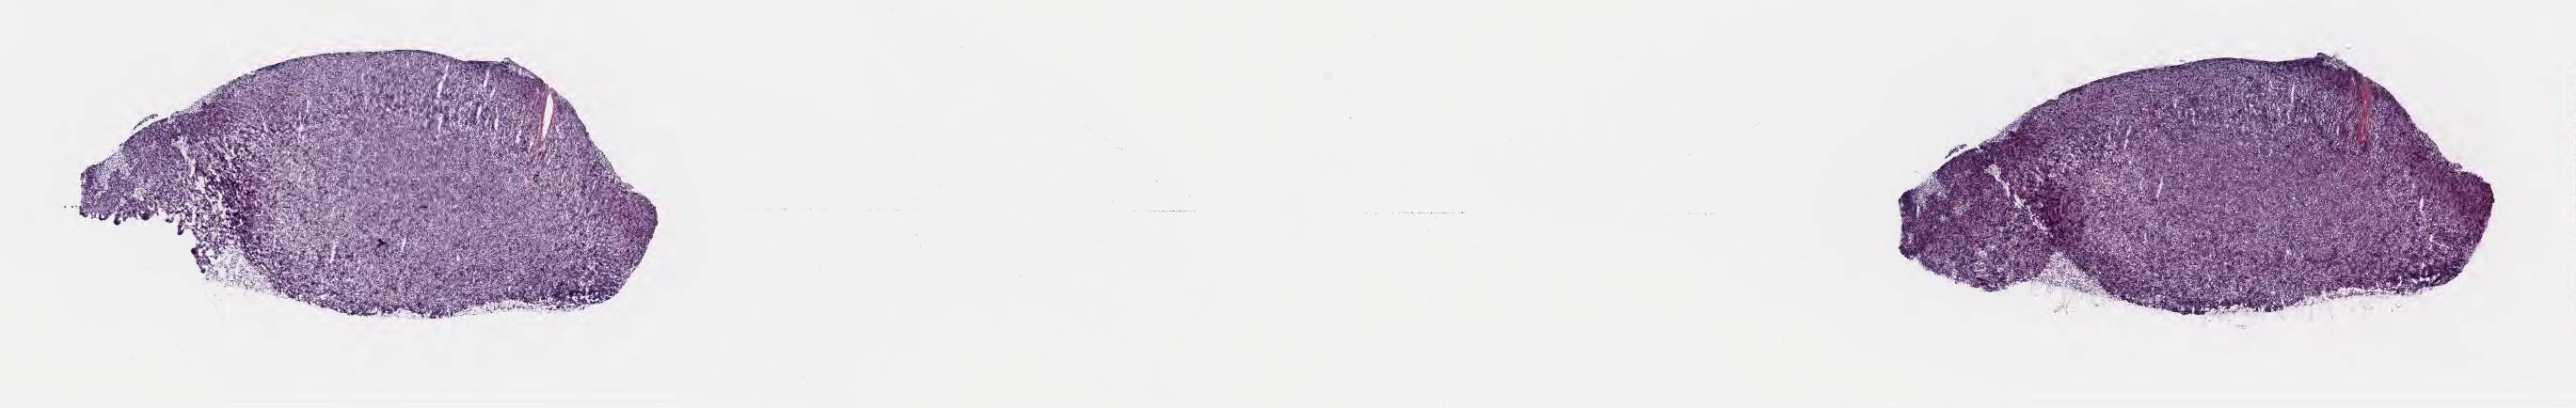
Whole-slide image, hematoxylin and eosin (H&E) stain, whole scanned area (about 22.1 x 3.5 mm) shown as a low-resolution overview; frozen section (tissue freezing medium); primary tumor; anatomic site: mandible. Male patient; age at initial diagnosis 8 years. Composition of this section per pathologist review: tumor cells 90%, tumor nuclei 90%, stromal cells 0%, necrosis 10%, normal cells 0%. Inflammatory infiltration, as recorded: lymphocyte infiltration 20%, monocyte infiltration 50%, neutrophil infiltration 10%.
• diagnosis: Burkitt lymphoma, NOS
• section: top of the tissue portion
• Ann Arbor stage (patient): Stage III